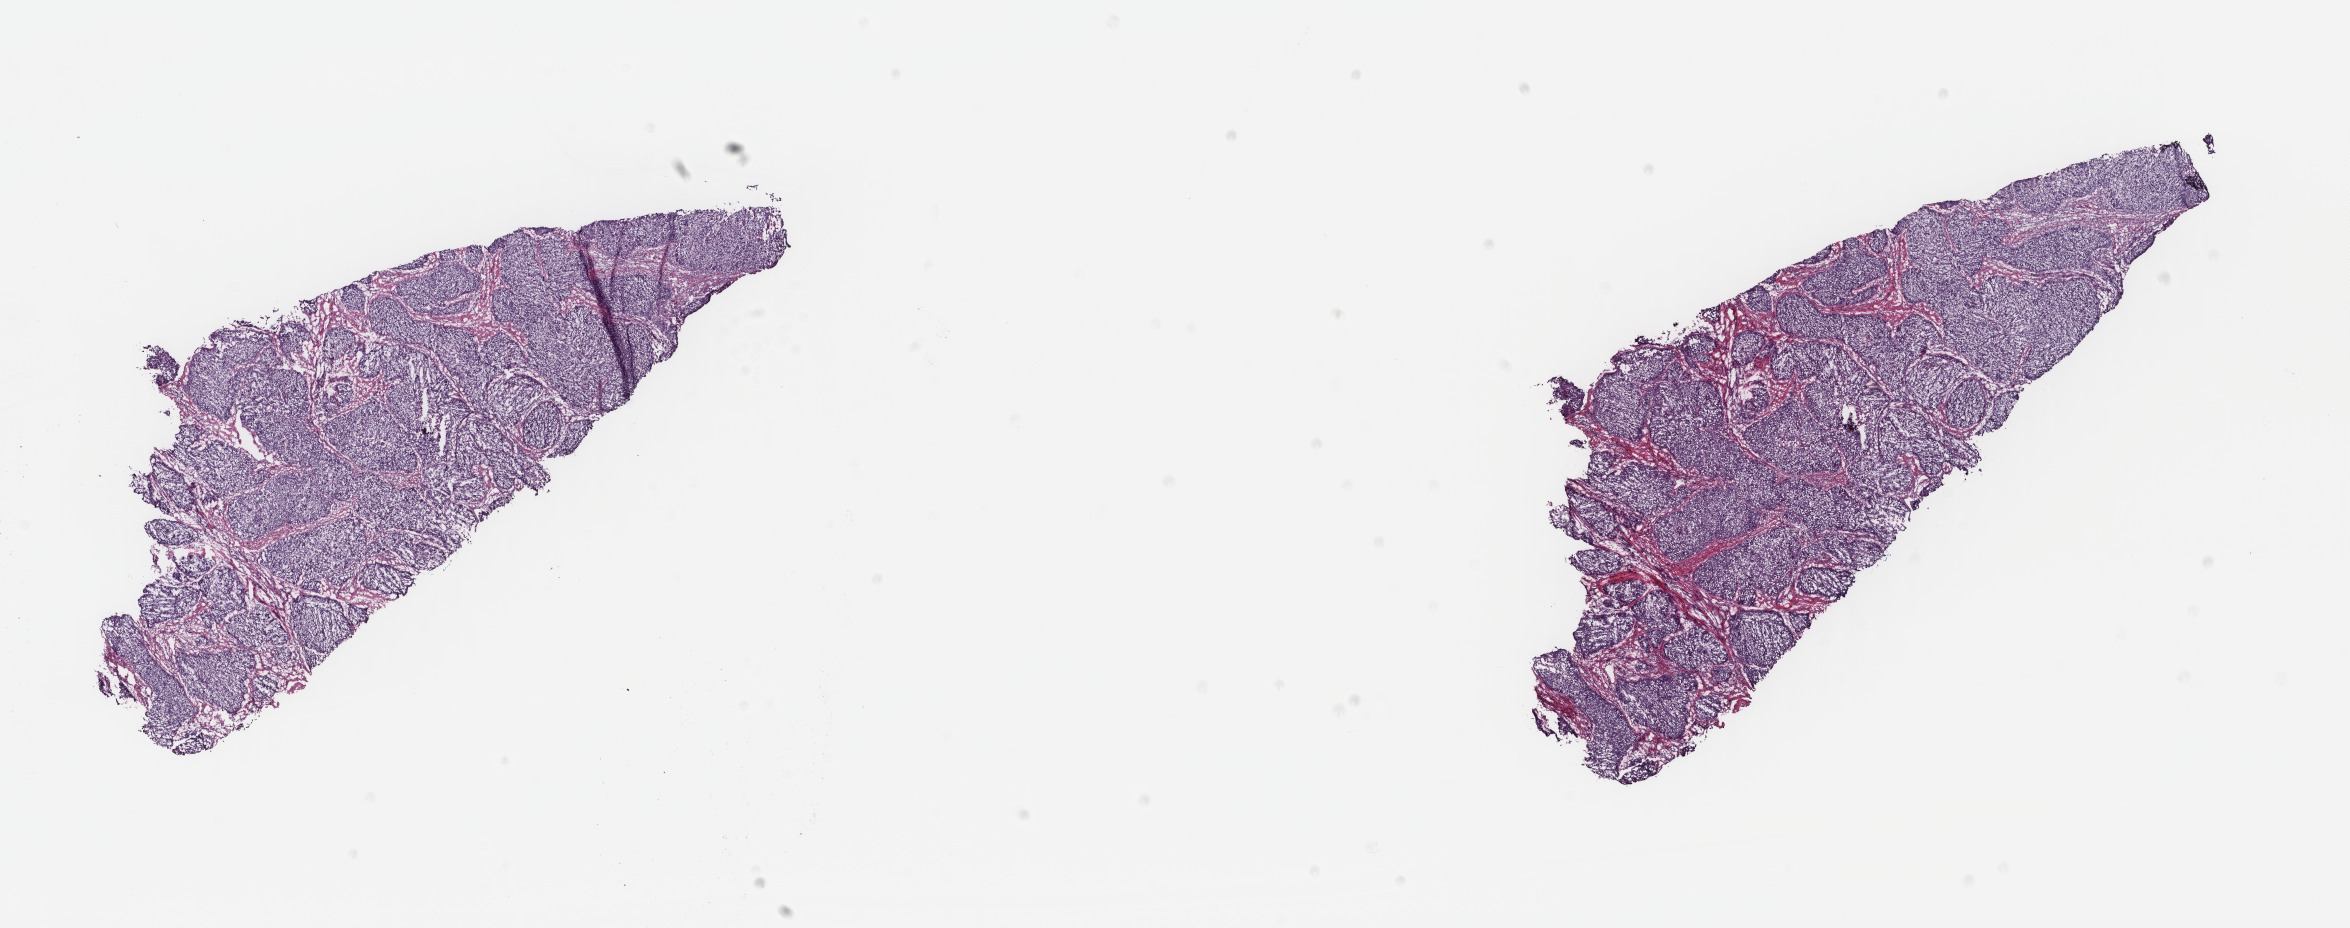
Whole-slide histology image, H&E, whole scanned area (about 18.7 x 7.4 mm) shown as a low-resolution overview, frozen section from the top of the tissue portion, primary tumour sample from the cervix. Patient: female, age at initial diagnosis 60 years. Histologic grade: G3 (poorly differentiated). Composition of this section per pathologist review: tumour cells 90%, tumour nuclei 90%, normal cells 0%, stromal cells 10%, necrosis 0%. Infiltration values recorded for this section: lymphocyte infiltration 40%, monocyte infiltration 20%, neutrophil infiltration 20%.
FIGO stage: IIA1. Diagnosis: Squamous cell carcinoma, NOS (cervix uteri).